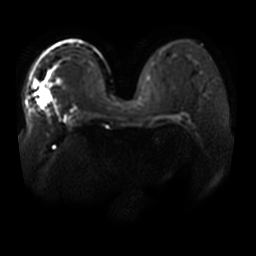
Breast MRI, one axial slice. Position 27 of 44 along the scan axis. Diffusion-weighted series; image 2 of 4 stored at this slice position (different b-values; order by instance number). 3 T. 5 mm slice thickness. 256 × 256 image matrix, field of view 400 × 400 mm. Female patient.
Structures marked on this image (manually delineated by an expert):
- tumour on diffusion-weighted imaging: box from (x=39, y=88) to (x=52, y=108) px